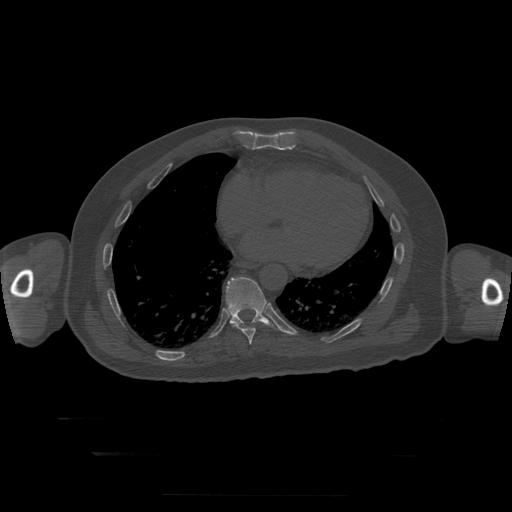
CT including the spine, one axial slice; position 134 of 397 along the scan axis; reconstruction kernel STANDARD; 120 kVp; bone window (W 1800 / L 400 HU); 1.25 mm slice thickness; 512 × 512 image matrix, field of view 510 × 510 mm. Patient age 73 years. Case-level facts recorded for this patient, not image findings: primary cancer: prostate.
Structures marked on this image (semi-automatically segmented with operator editing):
- T10 vertebra: bounding box [x1, y1, x2, y2] px = [226, 277, 281, 331]
- T9 vertebra: [237, 325, 256, 345]